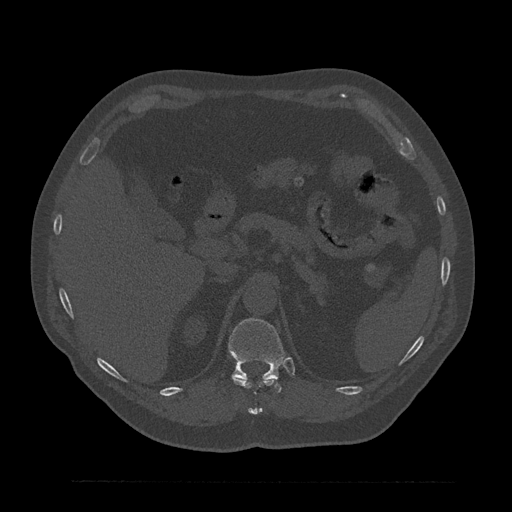
CT including the spine, one axial slice; slice 257 of 797 in the series (ordered by position); bone window (W 1800 / L 400 HU); 0.5 mm slice thickness; 512 × 512 image matrix, field of view 430 × 430 mm. Male patient, age 61 years. From the clinical record (not read from this slice): primary cancer: prostate.
Structures marked on this image (semi-automatic segmentation, software-assisted and operator-edited):
- T11 vertebra: box from (x=232, y=376) to (x=275, y=415) px
- T12 vertebra: (x=229, y=318)–(x=285, y=393)